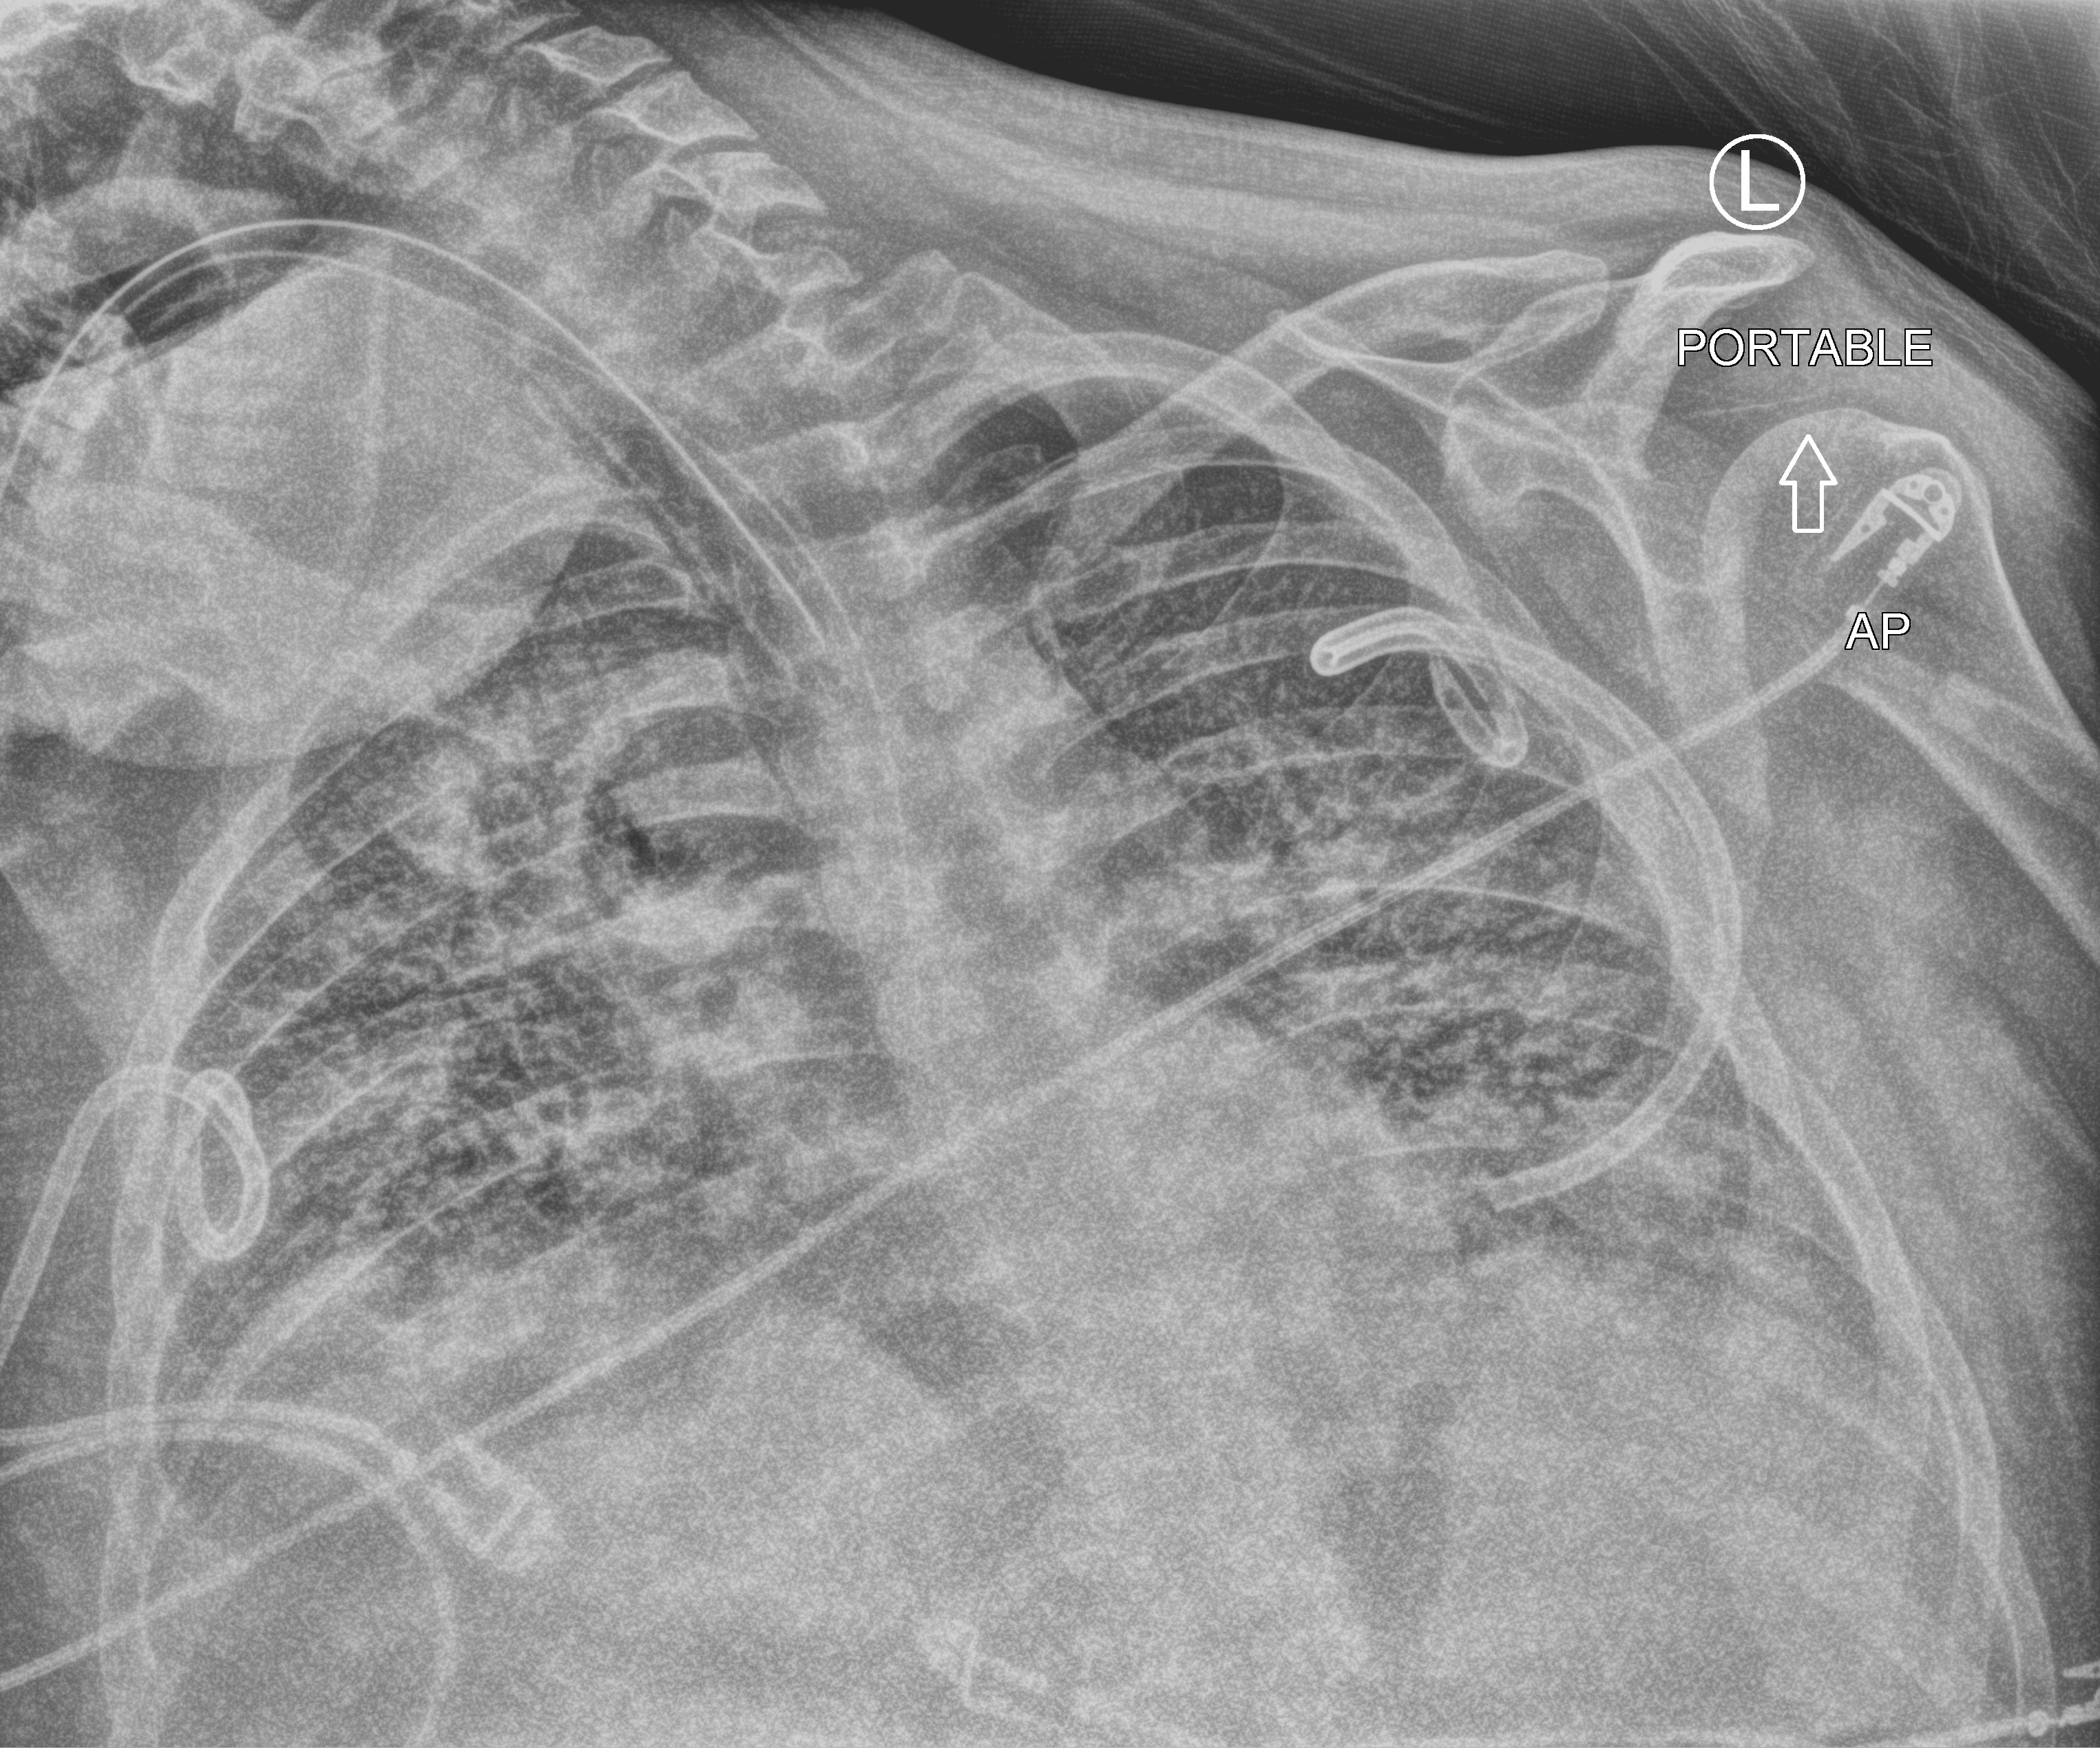
Portable chest radiograph, anteroposterior (AP) projection. Patient hospitalised with COVID-19, aged 18–59 years.
Admission-level facts for this patient (not findings on this image; timing relative to this image not recorded):
- mechanically ventilated during this hospital stay: yes